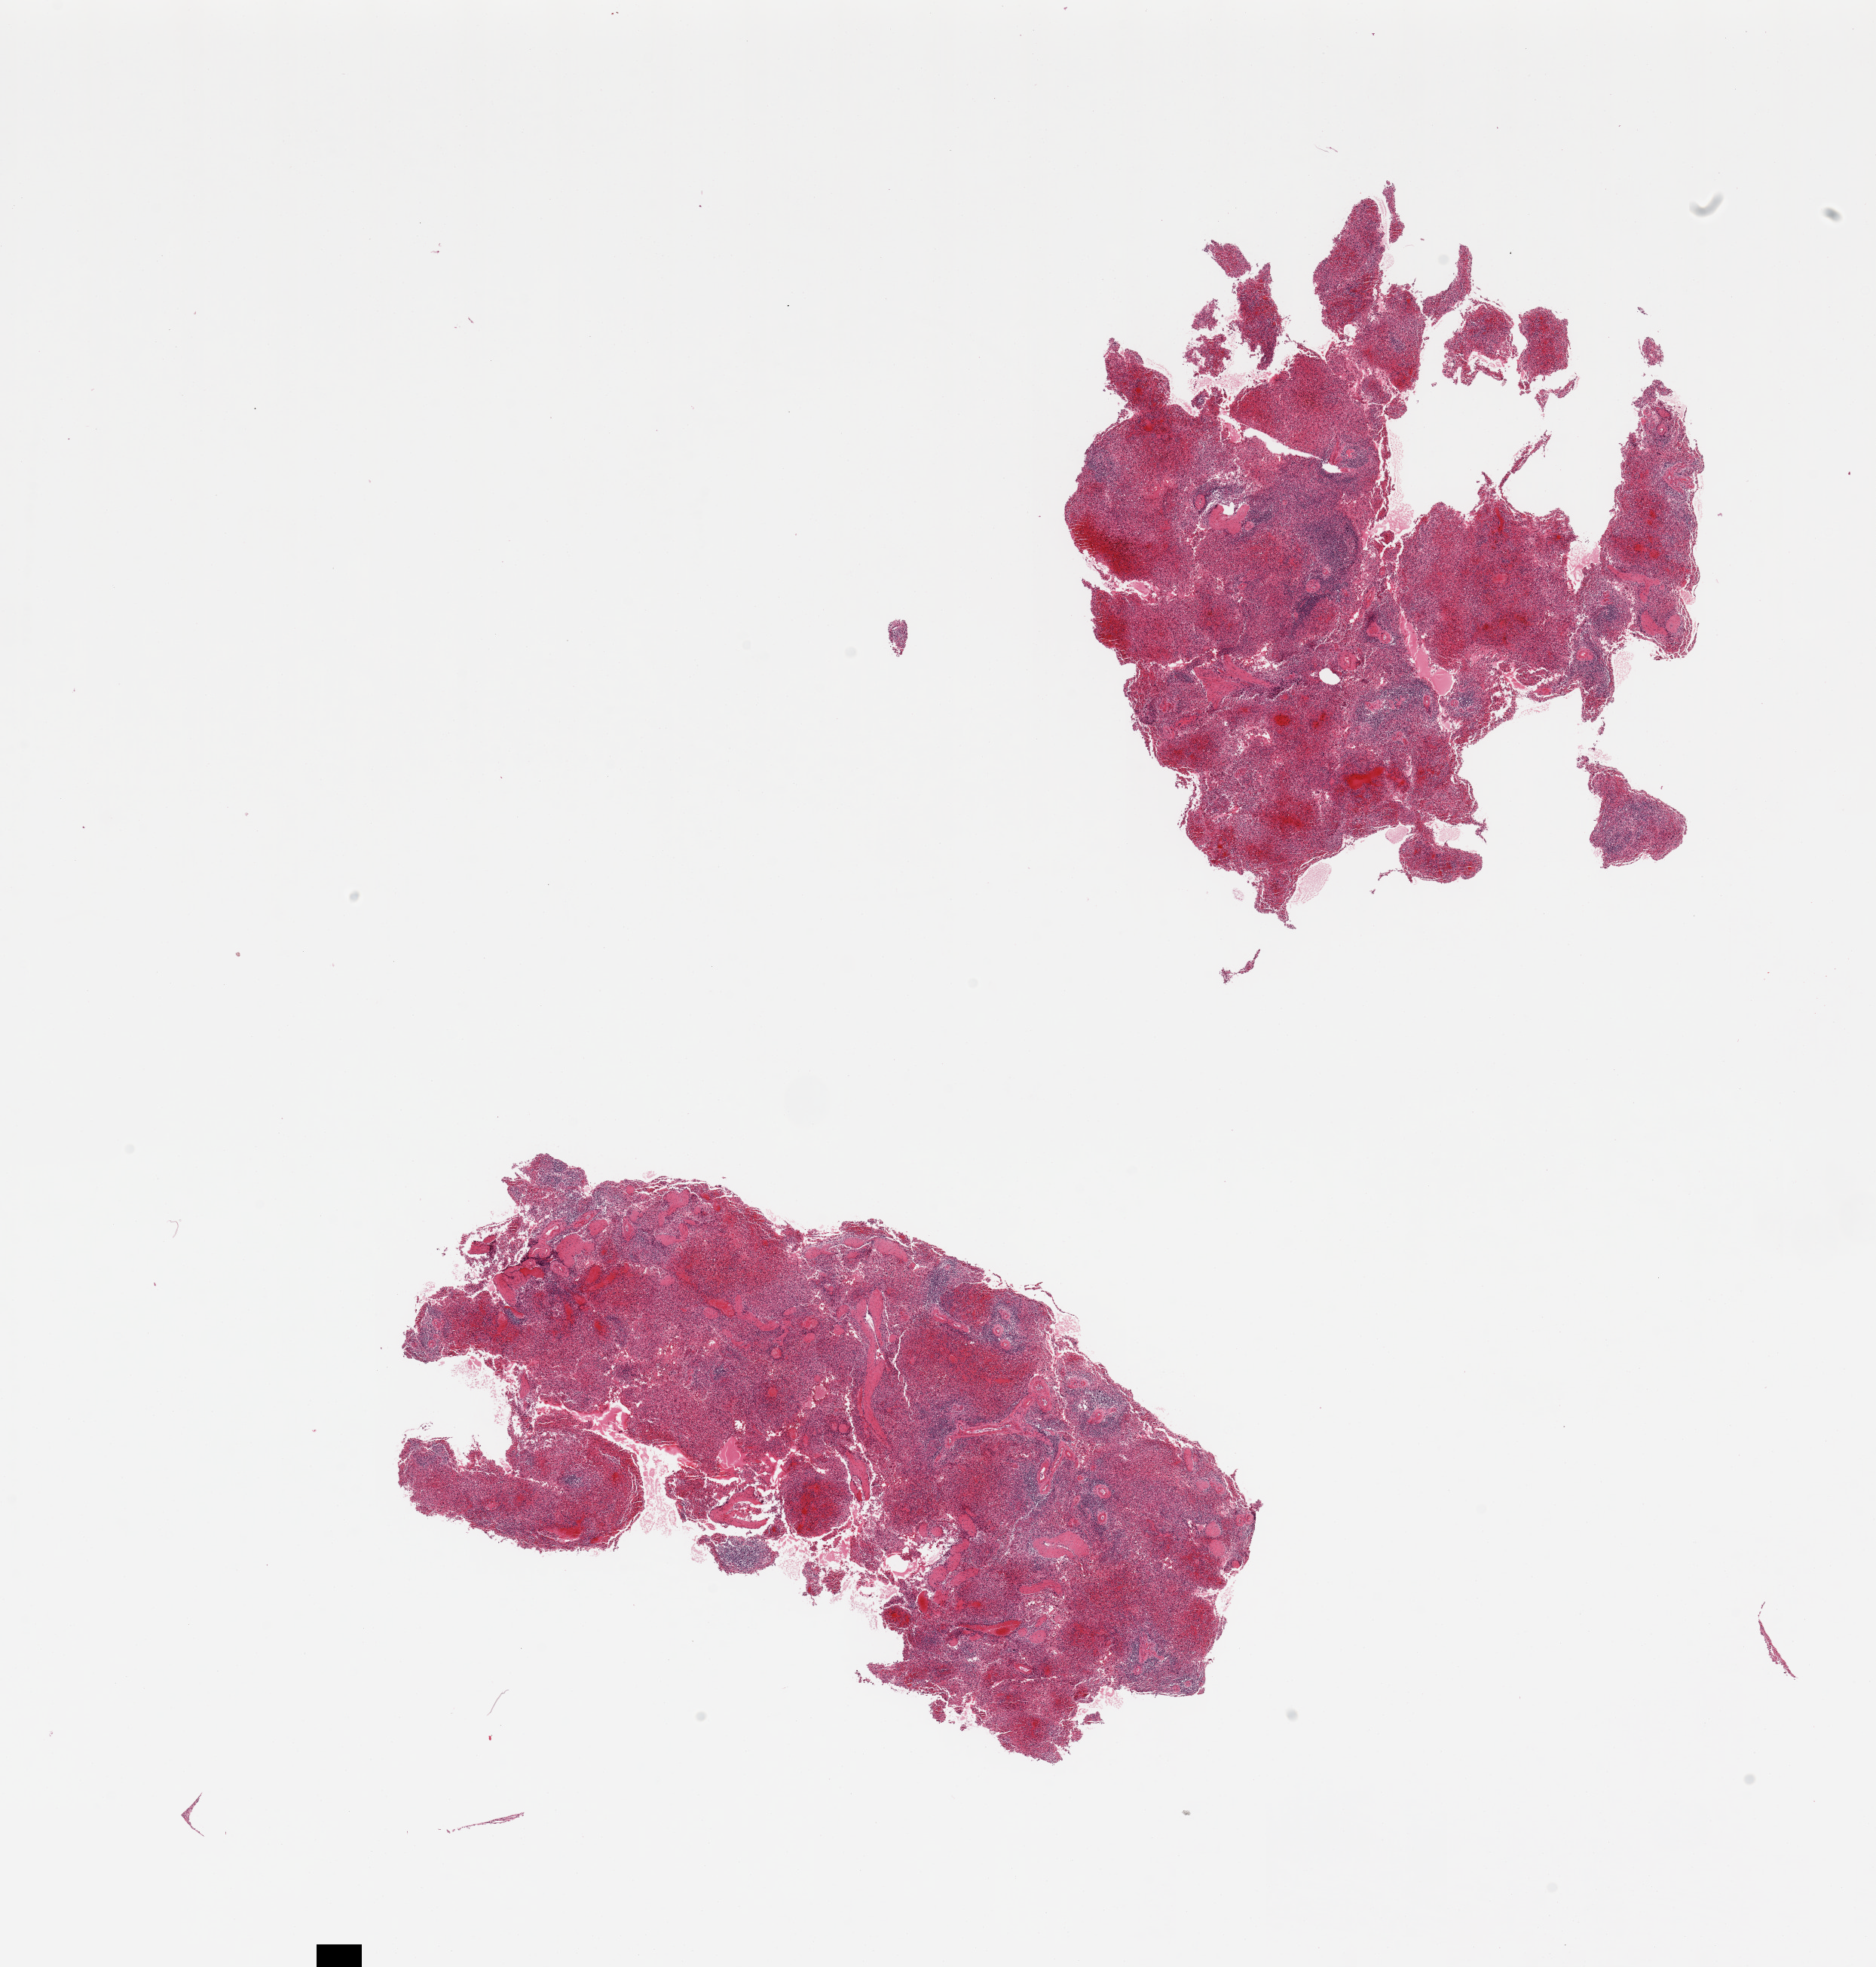
Whole-slide image, H&E stain, low-resolution overview of the scanned area, about 19.7 x 20.6 mm, PAXgene-fixed, paraffin-embedded tissue, target tissue: spleen, donor tissue sample. Donor: female.
- reviewer comment on this tissue sample: 2 pieces, congested